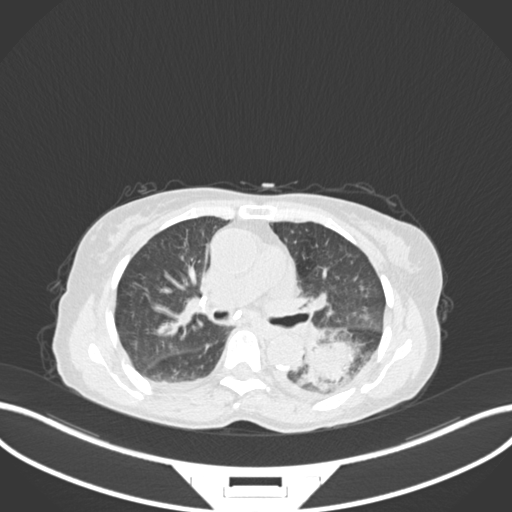
Chest CT, one axial slice. Slice 102 of 233 in the series (ordered by position). 120 kVp. Lung window (W 1500 / L -600 HU). 1 mm slice thickness. 512 × 512 image matrix, field of view 400 × 400 mm. Female patient, age 78 years. From the clinical record (not read from this slice): clinical TNM (as recorded): T3 N0 M1.
Outlined on this slice (rectangle marked by the reading radiologist):
- lung tumour (recorded histology: squamous cell carcinoma): box from (x=295, y=333) to (x=375, y=396) px